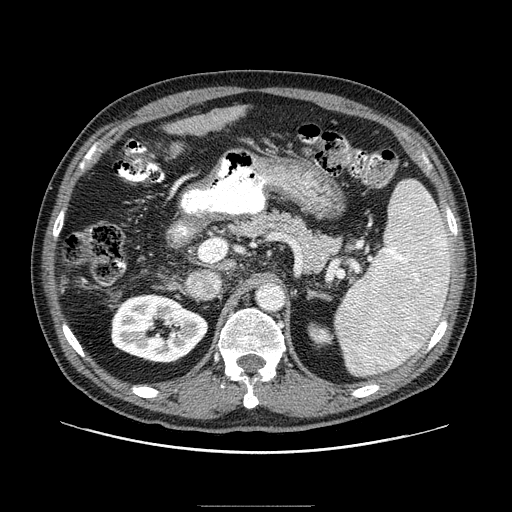
Contrast-enhanced abdominal CT (liver protocol), one axial slice. Slice 41 of 99 in the series (ordered by position). Reconstruction kernel STANDARD. 100 kVp. One of 2 acquisitions stored at this slice position. Soft-tissue window (W 400 / L 40 HU). 2.5 mm slice thickness. 512 × 512 image matrix, field of view 400 × 400 mm. From the clinical record (not read from this slice): diagnosis: hepatocellular carcinoma (patient treated with transarterial chemoembolisation; whether this scan precedes or follows treatment is not stated here); TNM stage (as recorded): Stage-II; Child-Pugh class: A.
Outlined on this slice (semi-automatically segmented with operator editing):
- liver parenchyma outside the tumour (the mass and vessels are separate outlines, so this box may not span the whole liver): bounding box (x1, y1, x2, y2) in pixels: (218, 106, 242, 124)